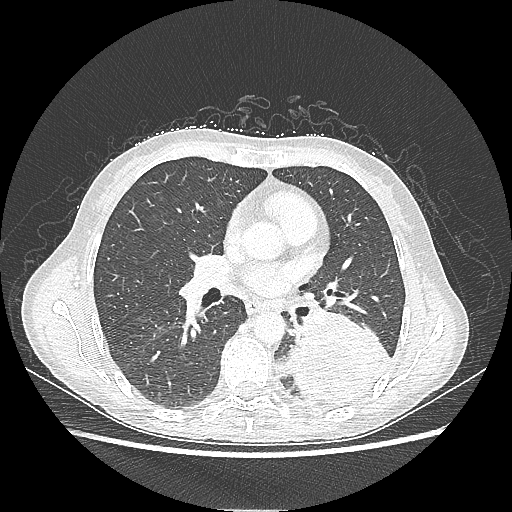
Chest CT, one axial slice; slice 117 of 220 in the series (ordered by position); reconstruction kernel LUNG; 80 kVp; lung window (W 1500 / L -600 HU); 1.25 mm slice thickness; 512 × 512 image matrix, field of view 360 × 360 mm. Patient: female, 53 years. From the clinical record (not read from this slice): clinical TNM (as recorded): T3 N0 M0.
Annotated regions visible in this slice (rectangle marked by the reading radiologist):
- lung tumour (recorded histology: adenocarcinoma): box from (x=288, y=311) to (x=391, y=403) px